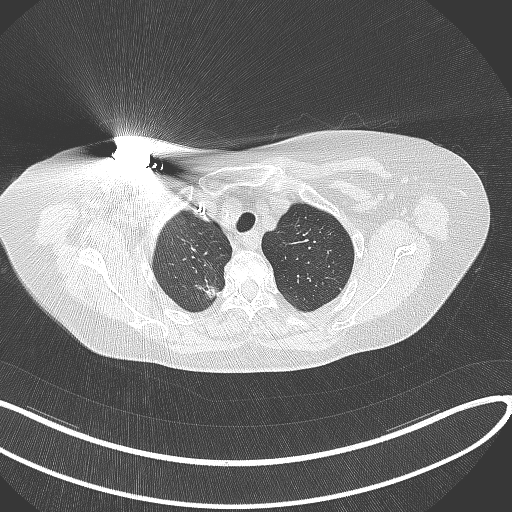
Chest CT, one axial slice; slice 283 of 316 in the series (ordered by position); 120 kVp; lung window (W 1500 / L -600 HU); 512 × 512 image matrix, field of view 400 × 400 mm. Female patient, age 72 years. From the clinical record (not read from this slice): clinical TNM (as recorded): T1c N0 M0.
Structures marked on this image (bounding box drawn by a radiologist):
- lung tumour (recorded histology: adenocarcinoma): box from (x=191, y=278) to (x=219, y=299) px